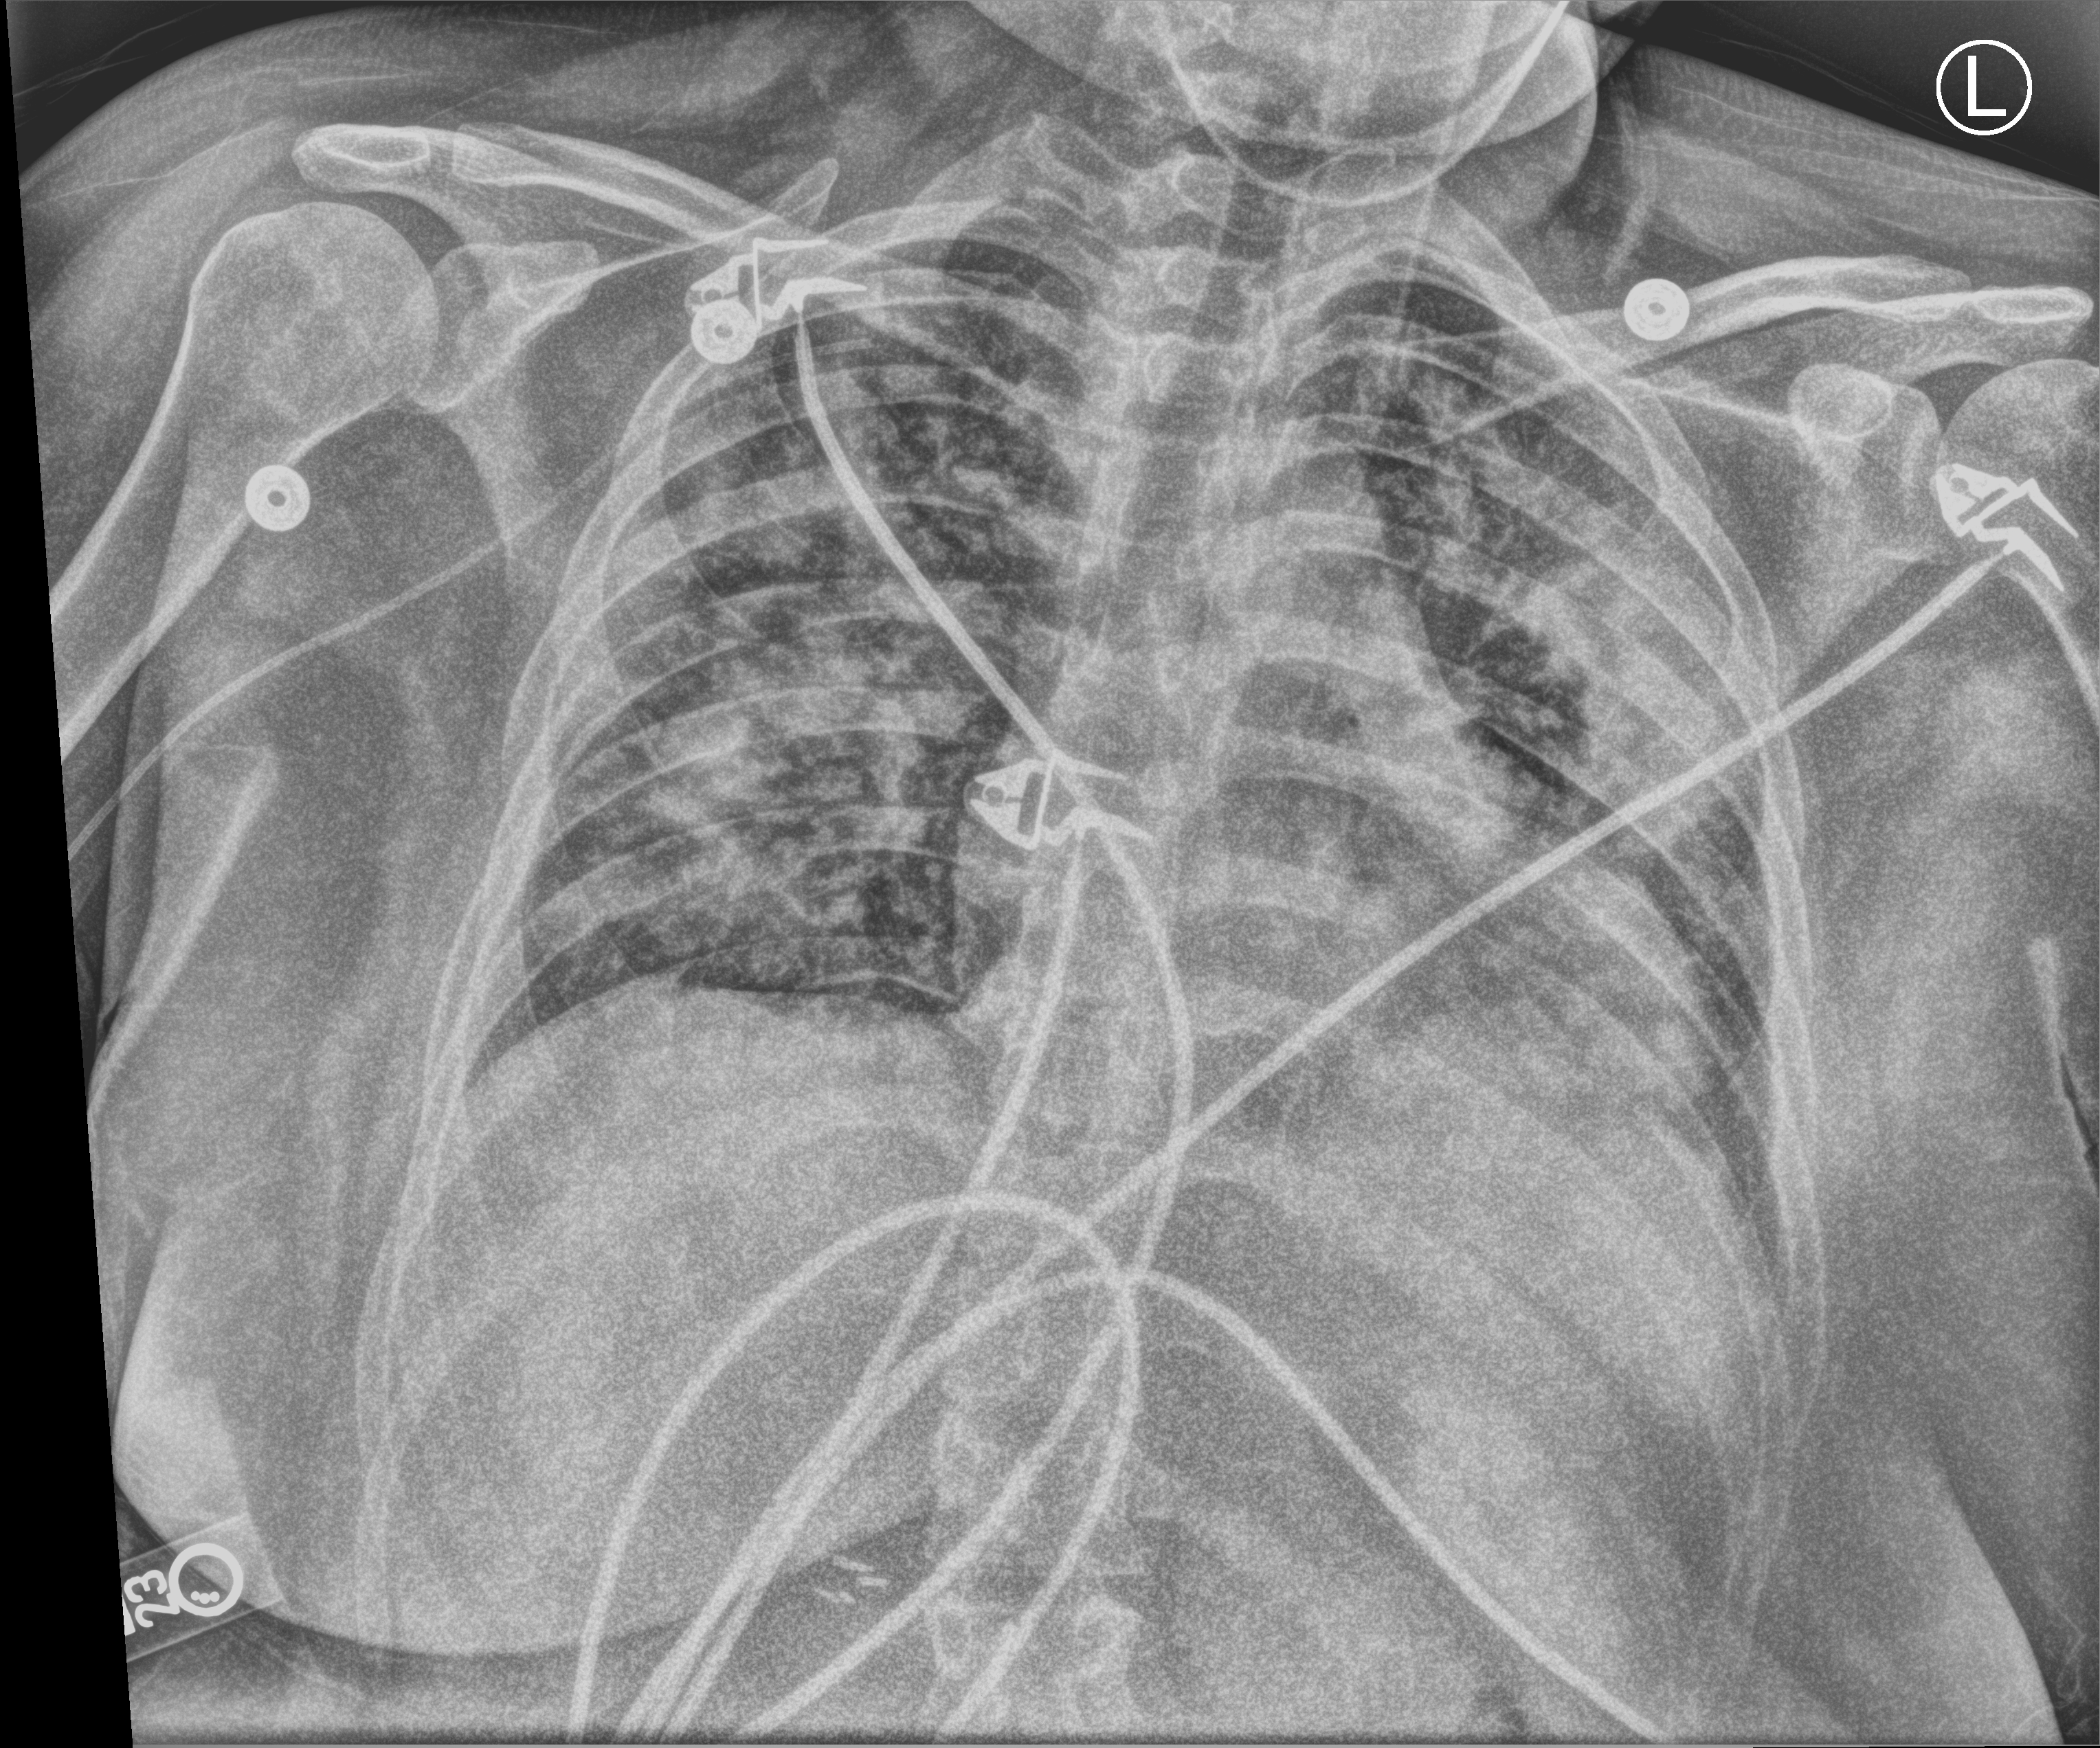
Portable chest radiograph. Female patient hospitalised with COVID-19, age 18–59 years.
From the hospital-stay record, not from the radiograph (when in the stay this image was taken is not recorded): diabetes (admission record): no.